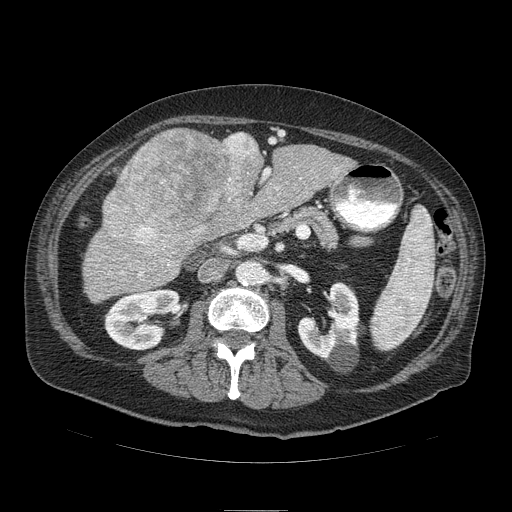
Contrast-enhanced abdominal CT (liver protocol), one axial slice; position 36 of 103 along the scan axis; soft-tissue window (W 400 / L 40 HU); 2.5 mm slice thickness; 512 × 512 image matrix. From the clinical record (not read from this slice): diagnosis: hepatocellular carcinoma (patient treated with transarterial chemoembolisation; whether this scan precedes or follows treatment is not stated here); TNM stage (as recorded): Stage-IIIA; Child-Pugh class: B; tumour differentiation: well differentiated; tumour nodularity: multinodular.
Structures marked on this image (semi-automatically segmented with operator editing):
- liver parenchyma outside the tumour (the mass and vessels are separate outlines, so this box may not span the whole liver): box from (x=84, y=128) to (x=355, y=298) px
- mass: (x=105, y=129)–(x=262, y=253)
- liver vessels: (x=121, y=133)–(x=270, y=276)